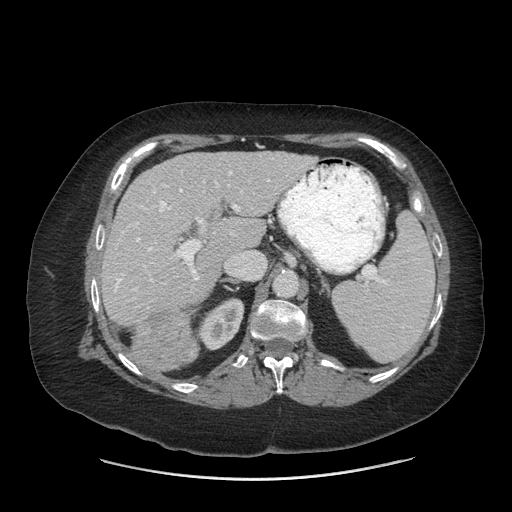
Contrast-enhanced abdominal CT (liver protocol), one axial slice; slice 41 of 69 in the series (ordered by position); reconstruction kernel STANDARD; 140 kVp; soft-tissue window (W 400 / L 40 HU); 512 × 512 image matrix, field of view 420 × 420 mm. From the clinical record (not read from this slice): diagnosis: hepatocellular carcinoma (patient treated with transarterial chemoembolisation; whether this scan precedes or follows treatment is not stated here); TNM stage (as recorded): Stage-IIIB; Child-Pugh class: A; tumour nodularity: multinodular.
Annotated regions visible in this slice (semi-automatic segmentation, software-assisted and operator-edited):
- liver parenchyma outside the tumour (the mass and vessels are separate outlines, so this box may not span the whole liver): box from (x=102, y=152) to (x=316, y=324) px
- mass: (x=128, y=305)–(x=199, y=371)
- liver vessels: (x=114, y=171)–(x=270, y=299)